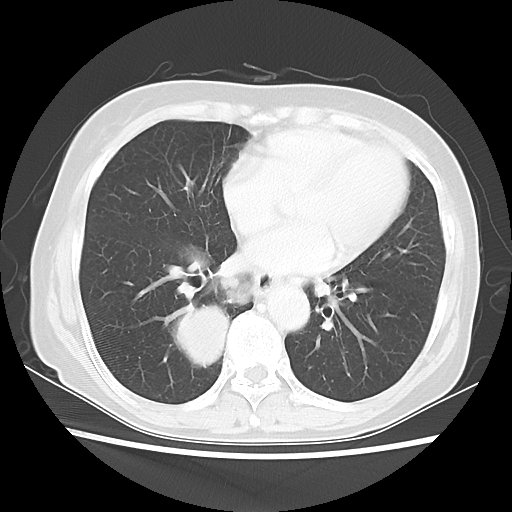
Chest CT, one axial slice; position 22 of 56 along the scan axis; reconstruction kernel LUNG; lung window (W 1500 / L -600 HU); 512 × 512 image matrix. Patient: female, 66 years. Case-level facts recorded for this patient, not image findings: clinical TNM (as recorded): T2 N3 M0; histopathological grade: G3.
Outlined on this slice (rectangle marked by the reading radiologist):
- lung tumour (recorded histology: small cell carcinoma): bounding box <164,295,232,367> (left, top, right, bottom; pixels)